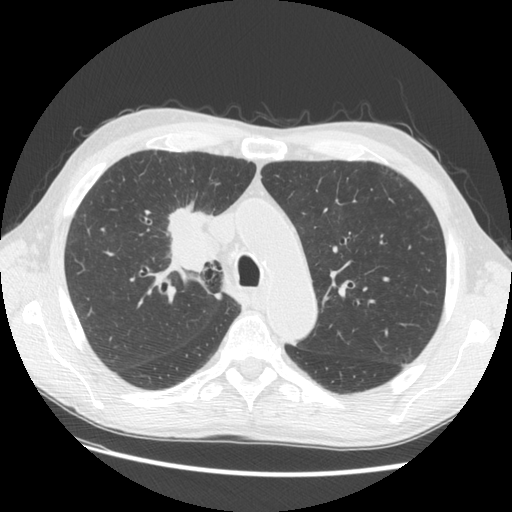
Low-dose screening chest CT, one axial slice; slice 96 of 133 in the series (ordered by position); reconstruction kernel STANDARD; 120 kVp; lung window (W 1500 / L -600 HU); 2.5 mm slice thickness; 512 × 512 image matrix, field of view 360 × 360 mm.
Annotated regions visible in this slice (expert manual segmentation):
- lesion 1 (tumor, hilum of right lung): box from (x=167, y=199) to (x=219, y=273) px